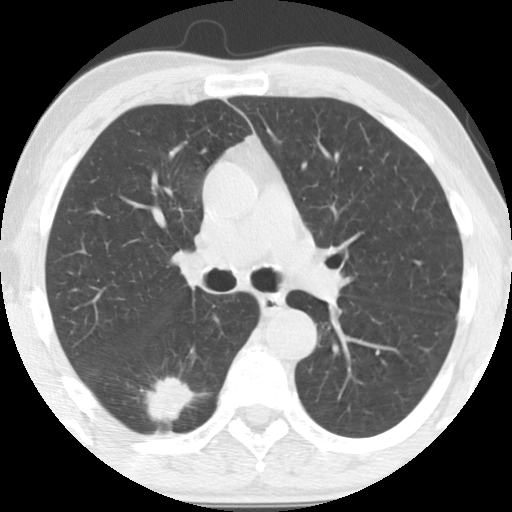
Axial slice from a low-dose chest CT screening exam; first (baseline) screen; lung window (W 1500 / L -600 HU); 2.5 mm slice thickness; 512 × 512 image matrix. Male participant, aged 64 years at enrolment. Current smoker at enrolment.
Expert-annotated lung lesion, box from (x=118, y=366) to (x=193, y=433) px. The exam's reader record, not a measurement of the box and not confirmed to be the same lesion: non-calcified nodule or mass ≥4 mm, right lower lobe, 36 × 26 mm, spiculated (stellate) margins, soft tissue attenuation. Official screen result: positive, change unspecified: nodule(s) >= 4 mm or enlarging nodule(s), mass(es), or other non-specific abnormalities suspicious for lung cancer. Later outcome: lung cancer diagnosed 20 days after this screen — adenocarcinoma, NOS, right lower lobe, moderately differentiated (G2), stage IA (AJCC 6th edition), 28 mm at pathology.